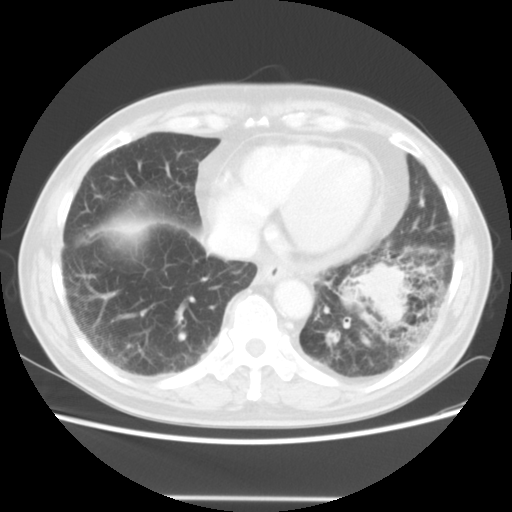
Chest CT, one axial slice; position 13 of 56 along the scan axis; reconstruction kernel STANDARD; 140 kVp; lung window (W 1500 / L -600 HU); 512 × 512 image matrix, field of view 360 × 360 mm. Male patient, age 66 years. From the clinical record (not read from this slice): clinical TNM (as recorded): T4 N3 M0; histopathological grade: G3.
Structures marked on this image (bounding box drawn by a radiologist):
- lung tumour (recorded histology: small cell carcinoma): bounding box (x1, y1, x2, y2) in pixels: (349, 260, 416, 334)